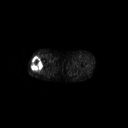
FDG PET of an extremity soft-tissue mass (from a PET/CT study), one axial slice; slice 242 of 267 in the series (ordered by position); 3.27 mm slice thickness; 128 × 128 image matrix, field of view 700 × 700 mm. Male patient, age 43 years. From the clinical record (not read from this slice): histological type: poorly differentiated synovial sarcoma; grade: high; site of the primary tumour: right buttock.
Annotated regions visible in this slice (expert contour drawn on MRI and transferred to this co-registered scan by the dataset authors):
- gross tumour volume including surrounding oedema: bounding box (x1, y1, x2, y2) in pixels: (31, 58, 43, 73)
- gross tumour volume (mass): (31, 58, 43, 73)